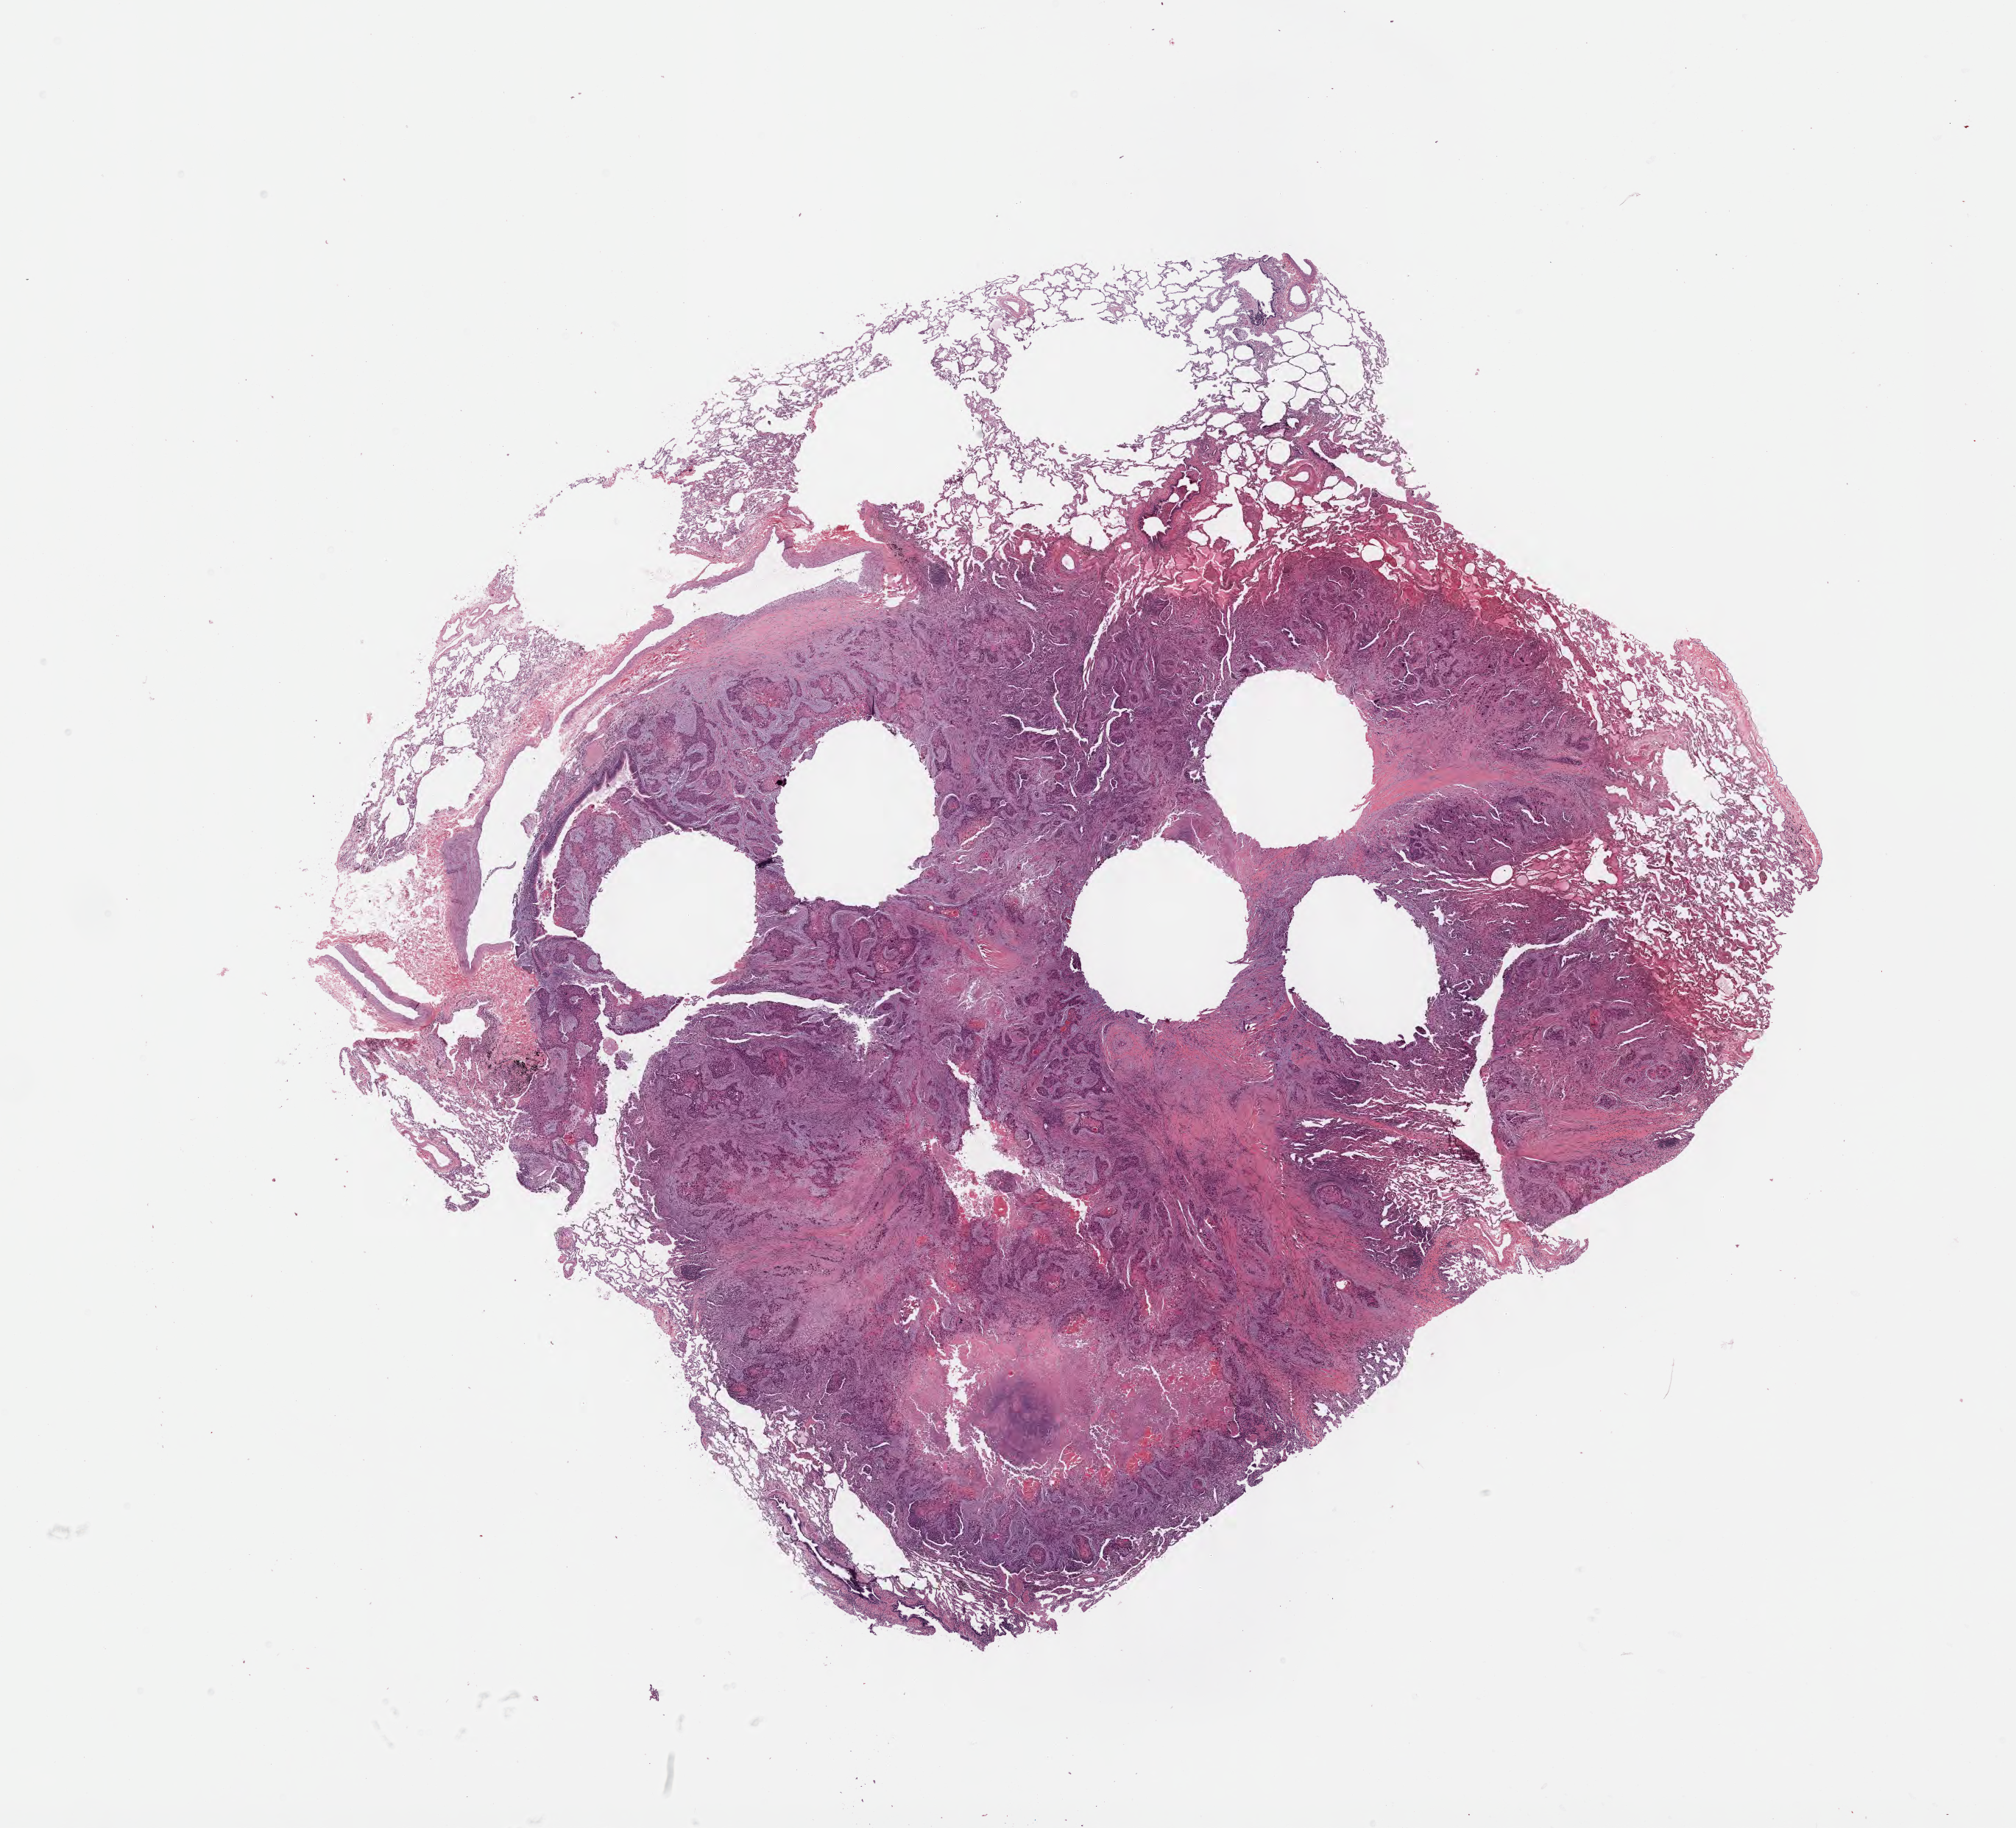
Digitized hematoxylin and eosin (H&E)-stained section, a low-resolution overview of the entire scanned area, about 22.1 x 20.1 mm. Male patient.
- specimen: tumor tissue; anatomic site: lower respiratory tract